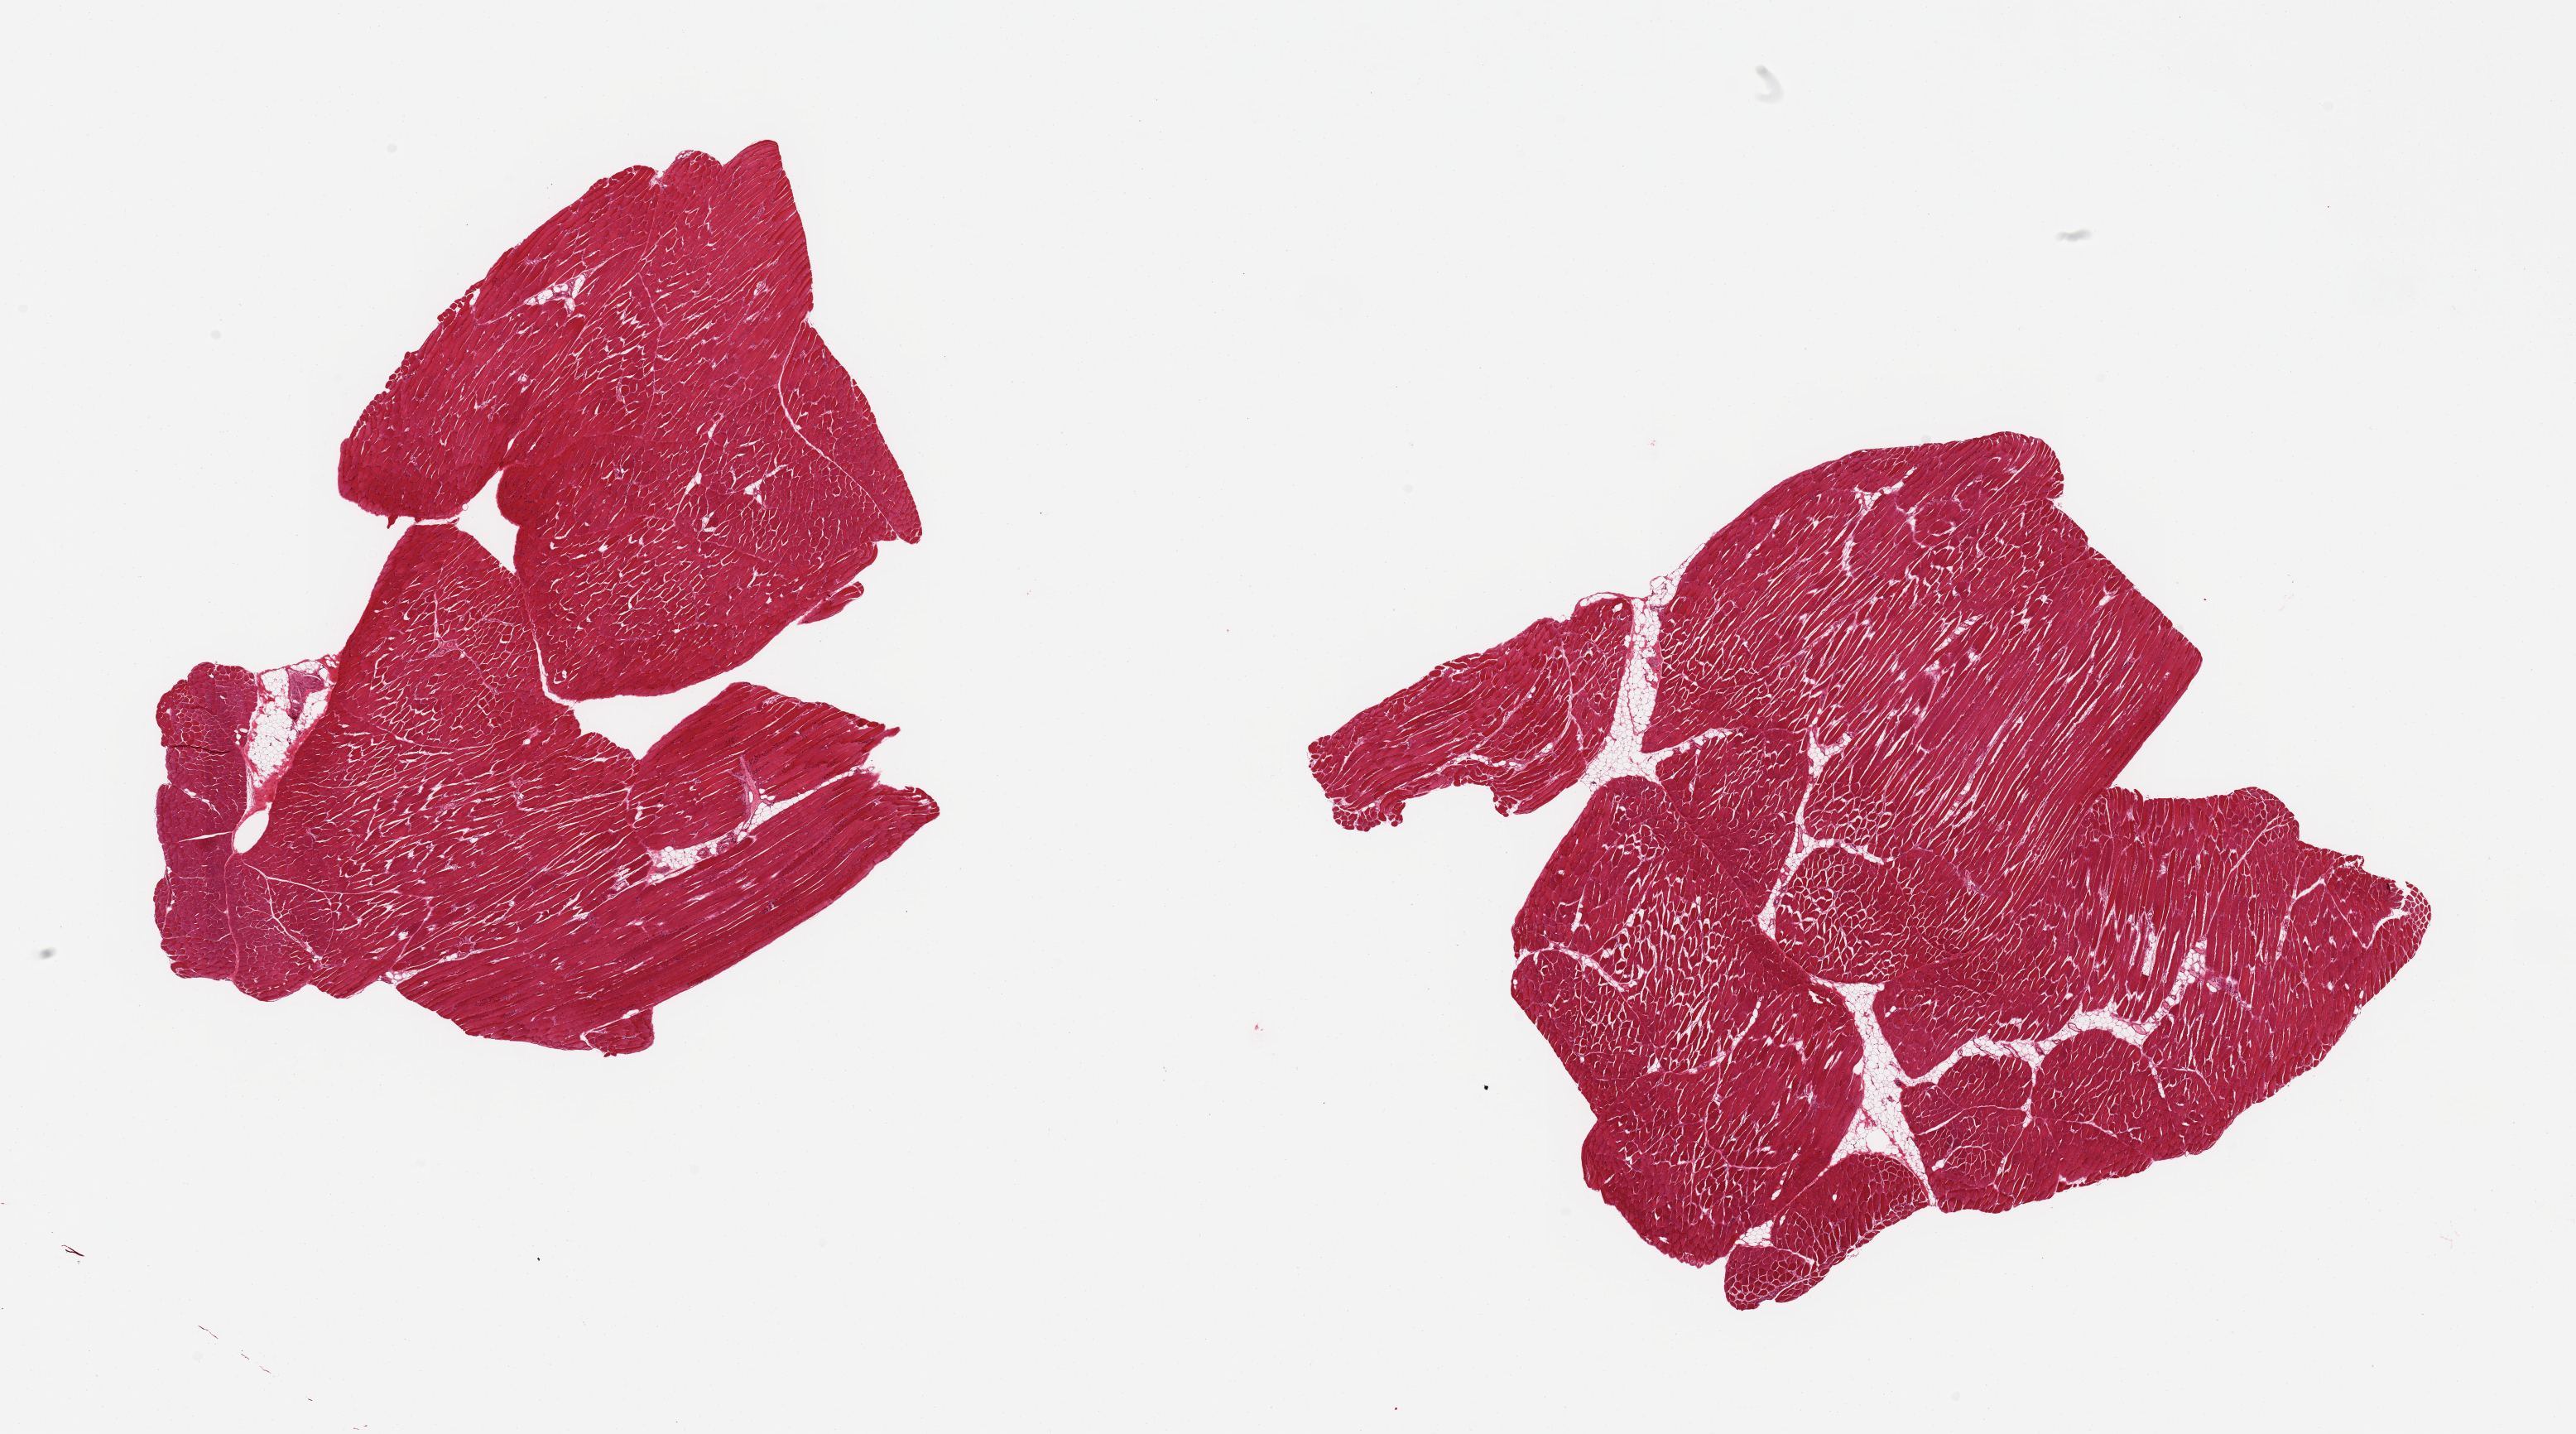
H&E whole-slide image, brightfield, low-resolution overview of the scanned area, about 24.6 x 13.7 mm (from a 20x scan), PAXgene-fixed, paraffin-embedded tissue, section of skeletal muscle (target tissue), tissue donor sample. Female donor.
Pathologist's review note for this sample: 2 pieces; includes minimal internal fat/nerve.